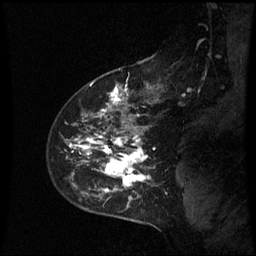
Breast MRI (dynamic contrast-enhanced), one sagittal slice. Slice 45 of 60 in the series (ordered by position). Dynamic contrast-enhanced series, image 2 of 3 at this slice position (ordered by acquisition). 1.5 T. TE 4.2 ms, TR 8.9 ms. 2.3 mm slice thickness. 256 × 256 image matrix. Patient: female, 43 years. Case-level facts recorded for this patient, not image findings: setting: breast cancer imaged before/during neoadjuvant chemotherapy; receptor status: HER2-positive.
Structures marked on this image (semi-automatic segmentation, software-assisted and operator-edited):
- analysis volume of interest (the breast-tissue region the enhancement analysis was run in; not a lesion): bounding box (x1, y1, x2, y2) in pixels: (57, 80, 162, 195)
- tumour enhancement mask (voxels above the 70 % enhancement threshold inside the analysis volume of interest): (70, 87, 151, 193)